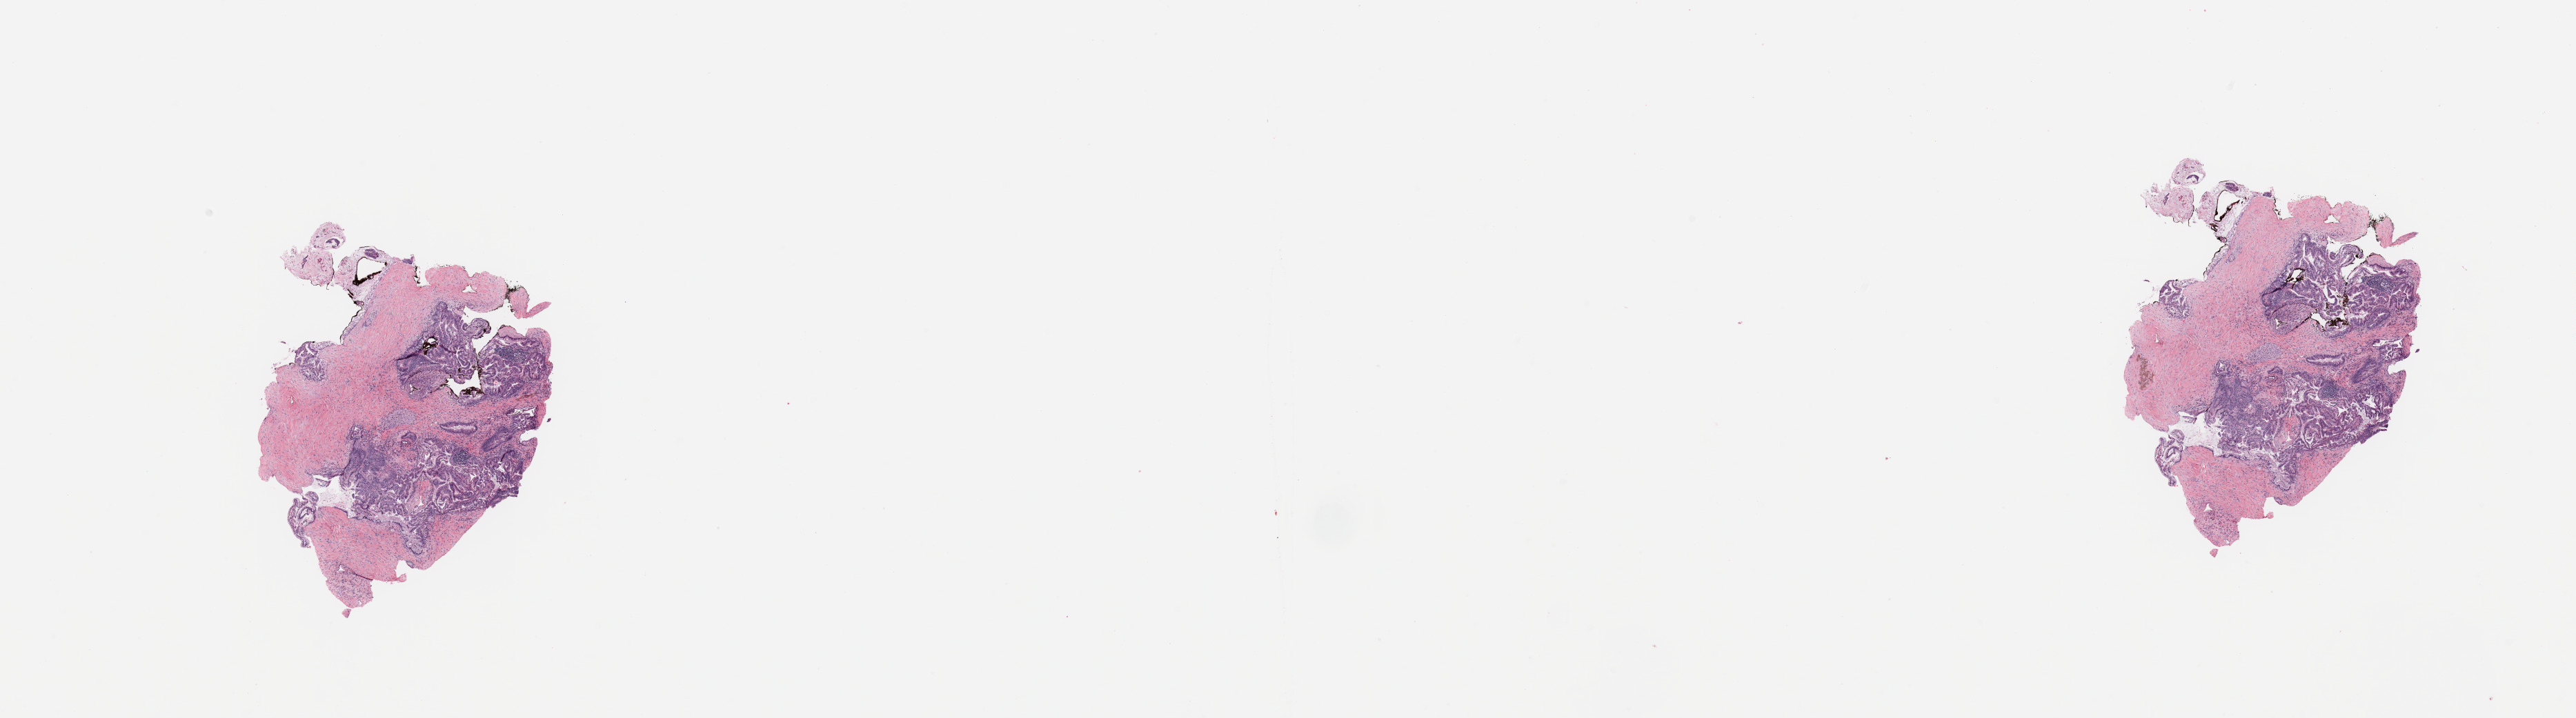
Whole-slide histology image, H&E — whole scanned area (about 29.5 x 8.2 mm) shown as a low-resolution overview, tumour tissue sample, sampled site: pancreas. Male, 67 y/o. Histologic grade: G2 (moderately differentiated). Pathologist review of this section (percent, as recorded): tumour nuclei 50%, necrosis 0%.
* AJCC pathologic stage: IB
* diagnosis: Infiltrating duct carcinoma, NOS